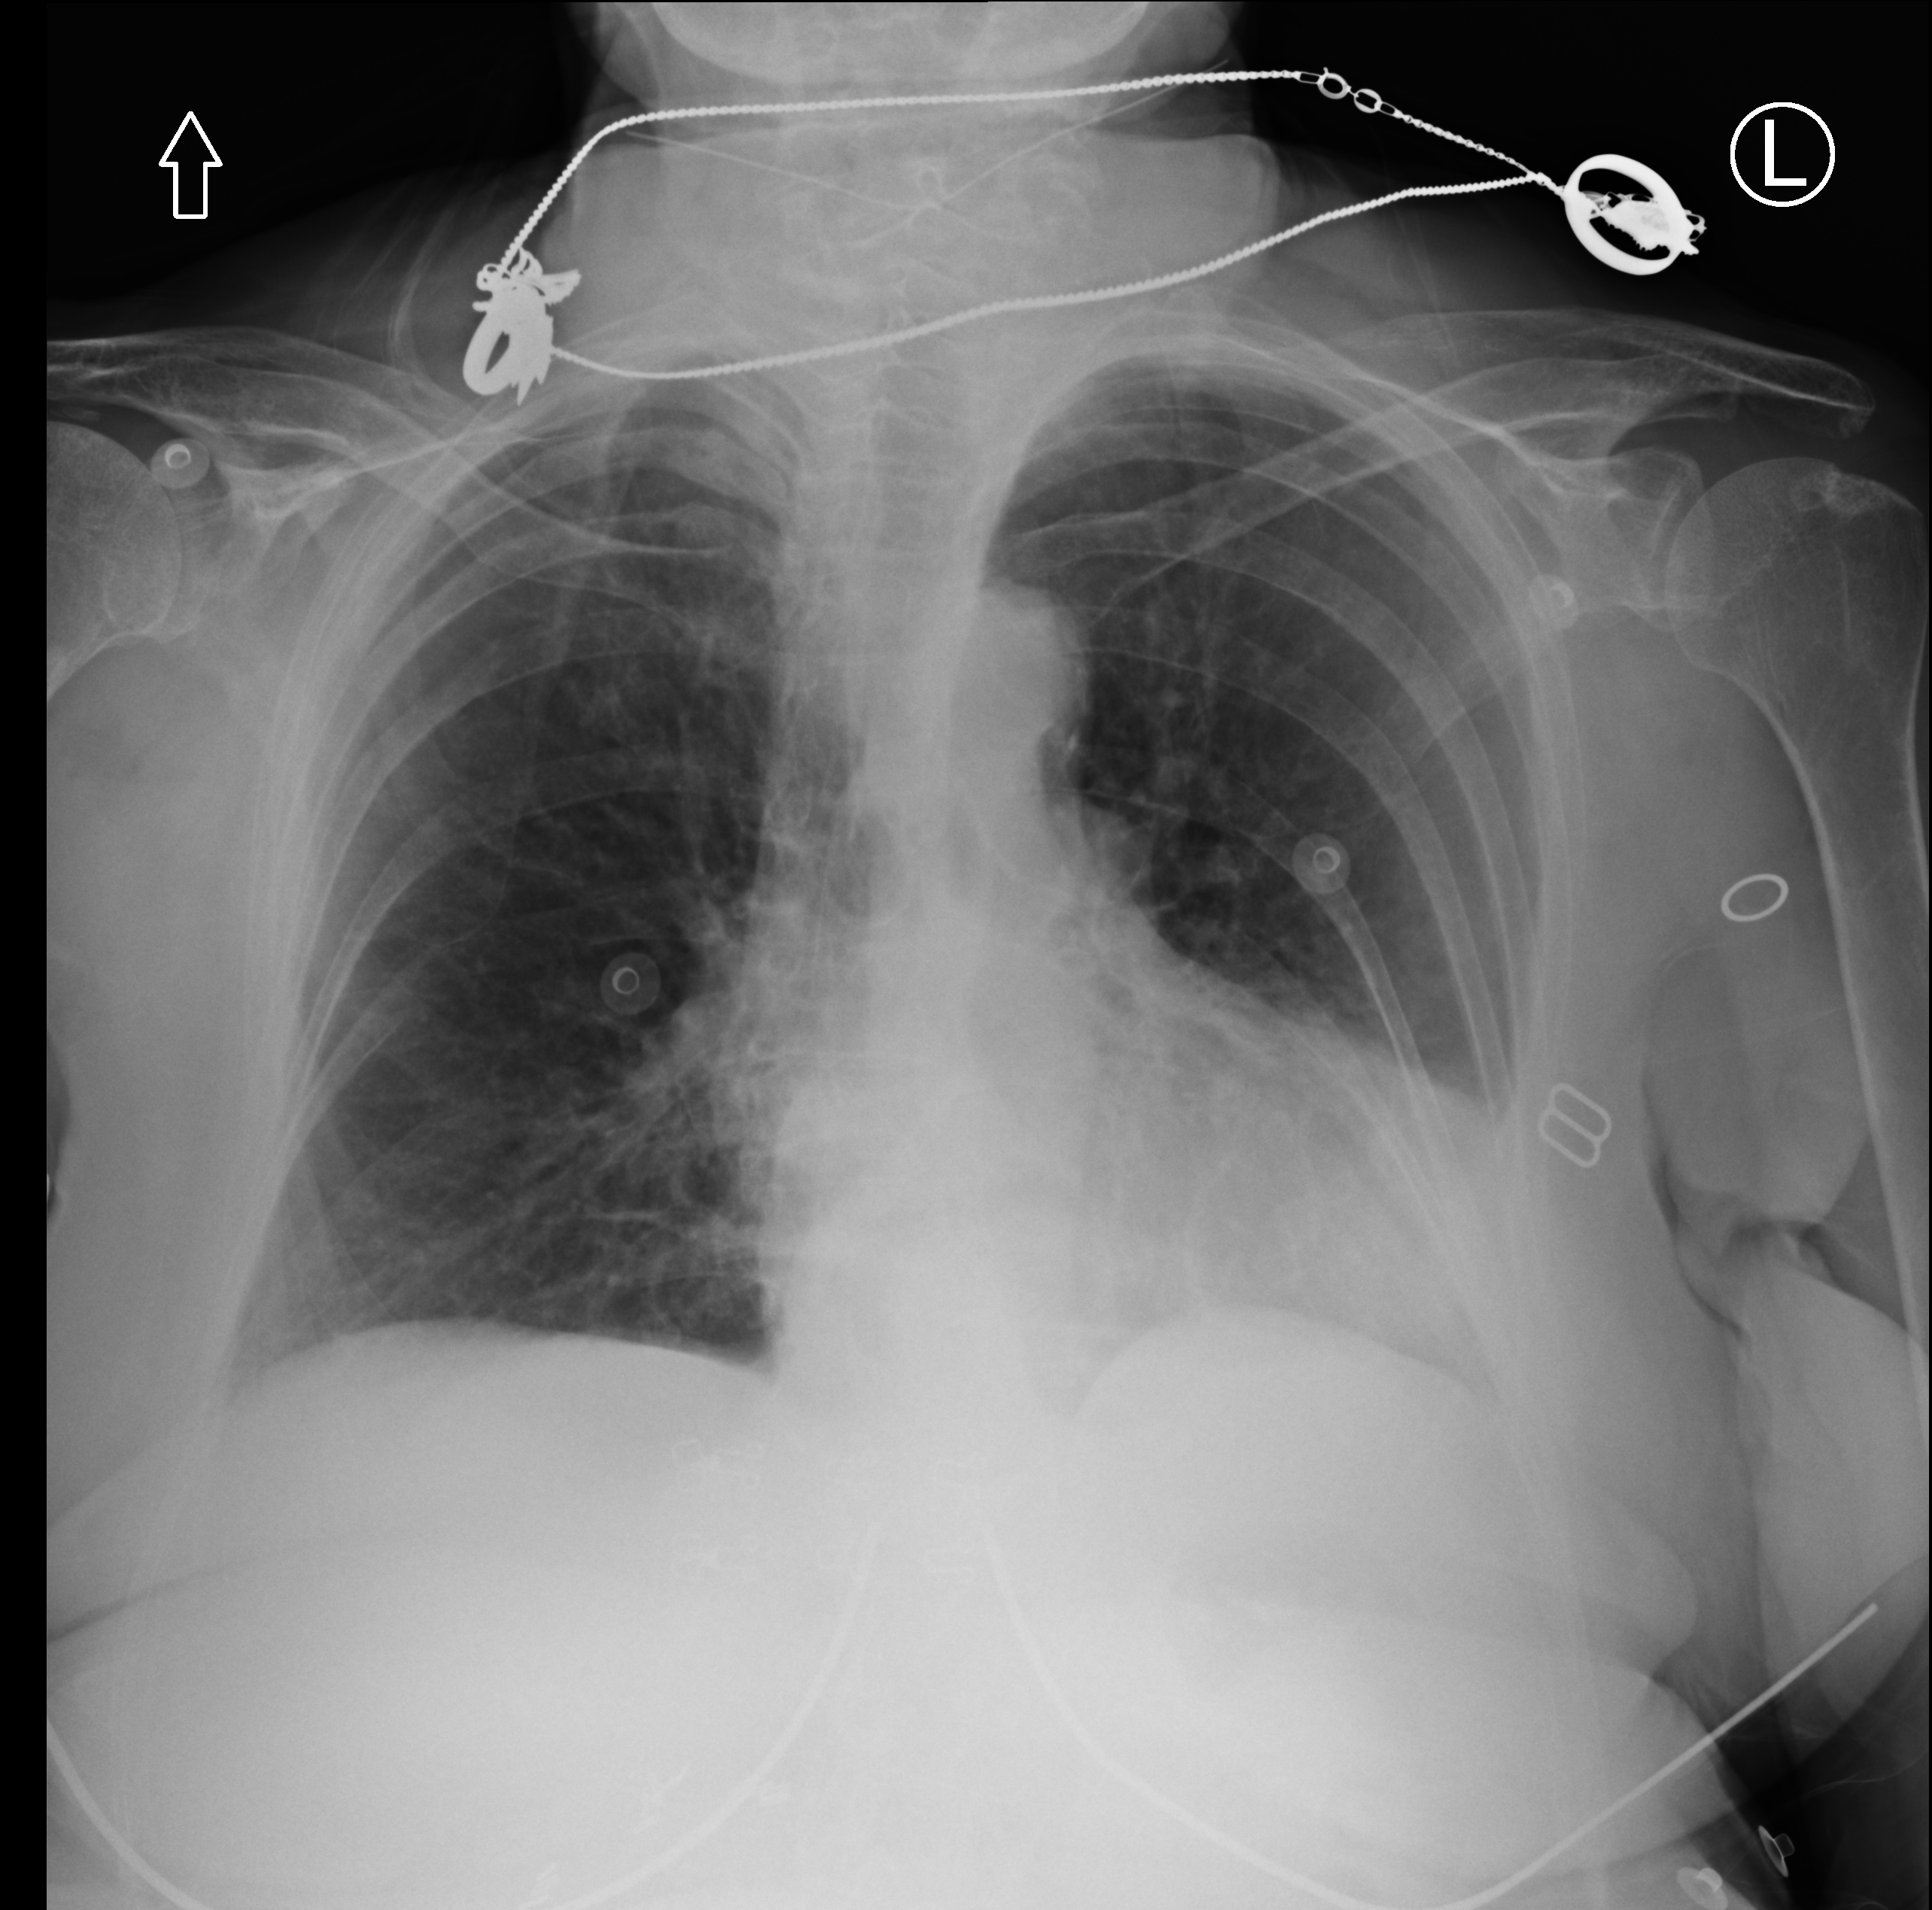
Bedside chest radiograph (computed radiography); anteroposterior (AP) projection. Female patient hospitalised with COVID-19, age 75–90 years.
From the hospital-stay record, not from the radiograph (when in the stay this image was taken is not recorded):
- admitted to intensive care during this hospital stay: no
- smoking status (admission record): never
- mechanically ventilated during this hospital stay: no